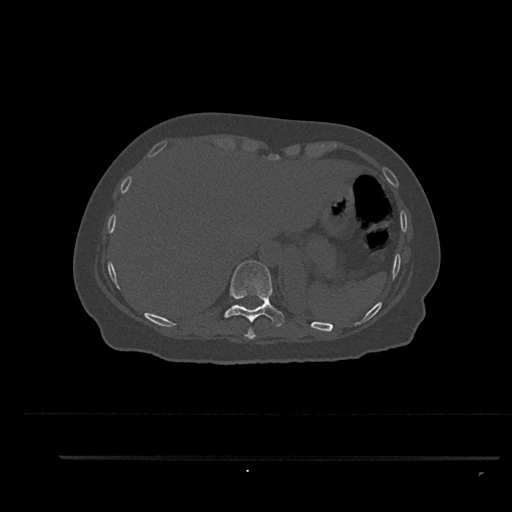
CT including the spine, one axial slice. Position 366 of 797 along the scan axis. Bone window (W 1800 / L 400 HU). 0.5 mm slice thickness. 512 × 512 image matrix. Patient: female, 44 years. From the clinical record (not read from this slice): primary cancer: renal; vertebrae with lytic lesions (as recorded): L1.
Structures marked on this image (semi-automatic segmentation, software-assisted and operator-edited):
- T10 vertebra: bounding box [x1, y1, x2, y2] px = [224, 260, 284, 333]
- T9 vertebra: [244, 328, 256, 339]